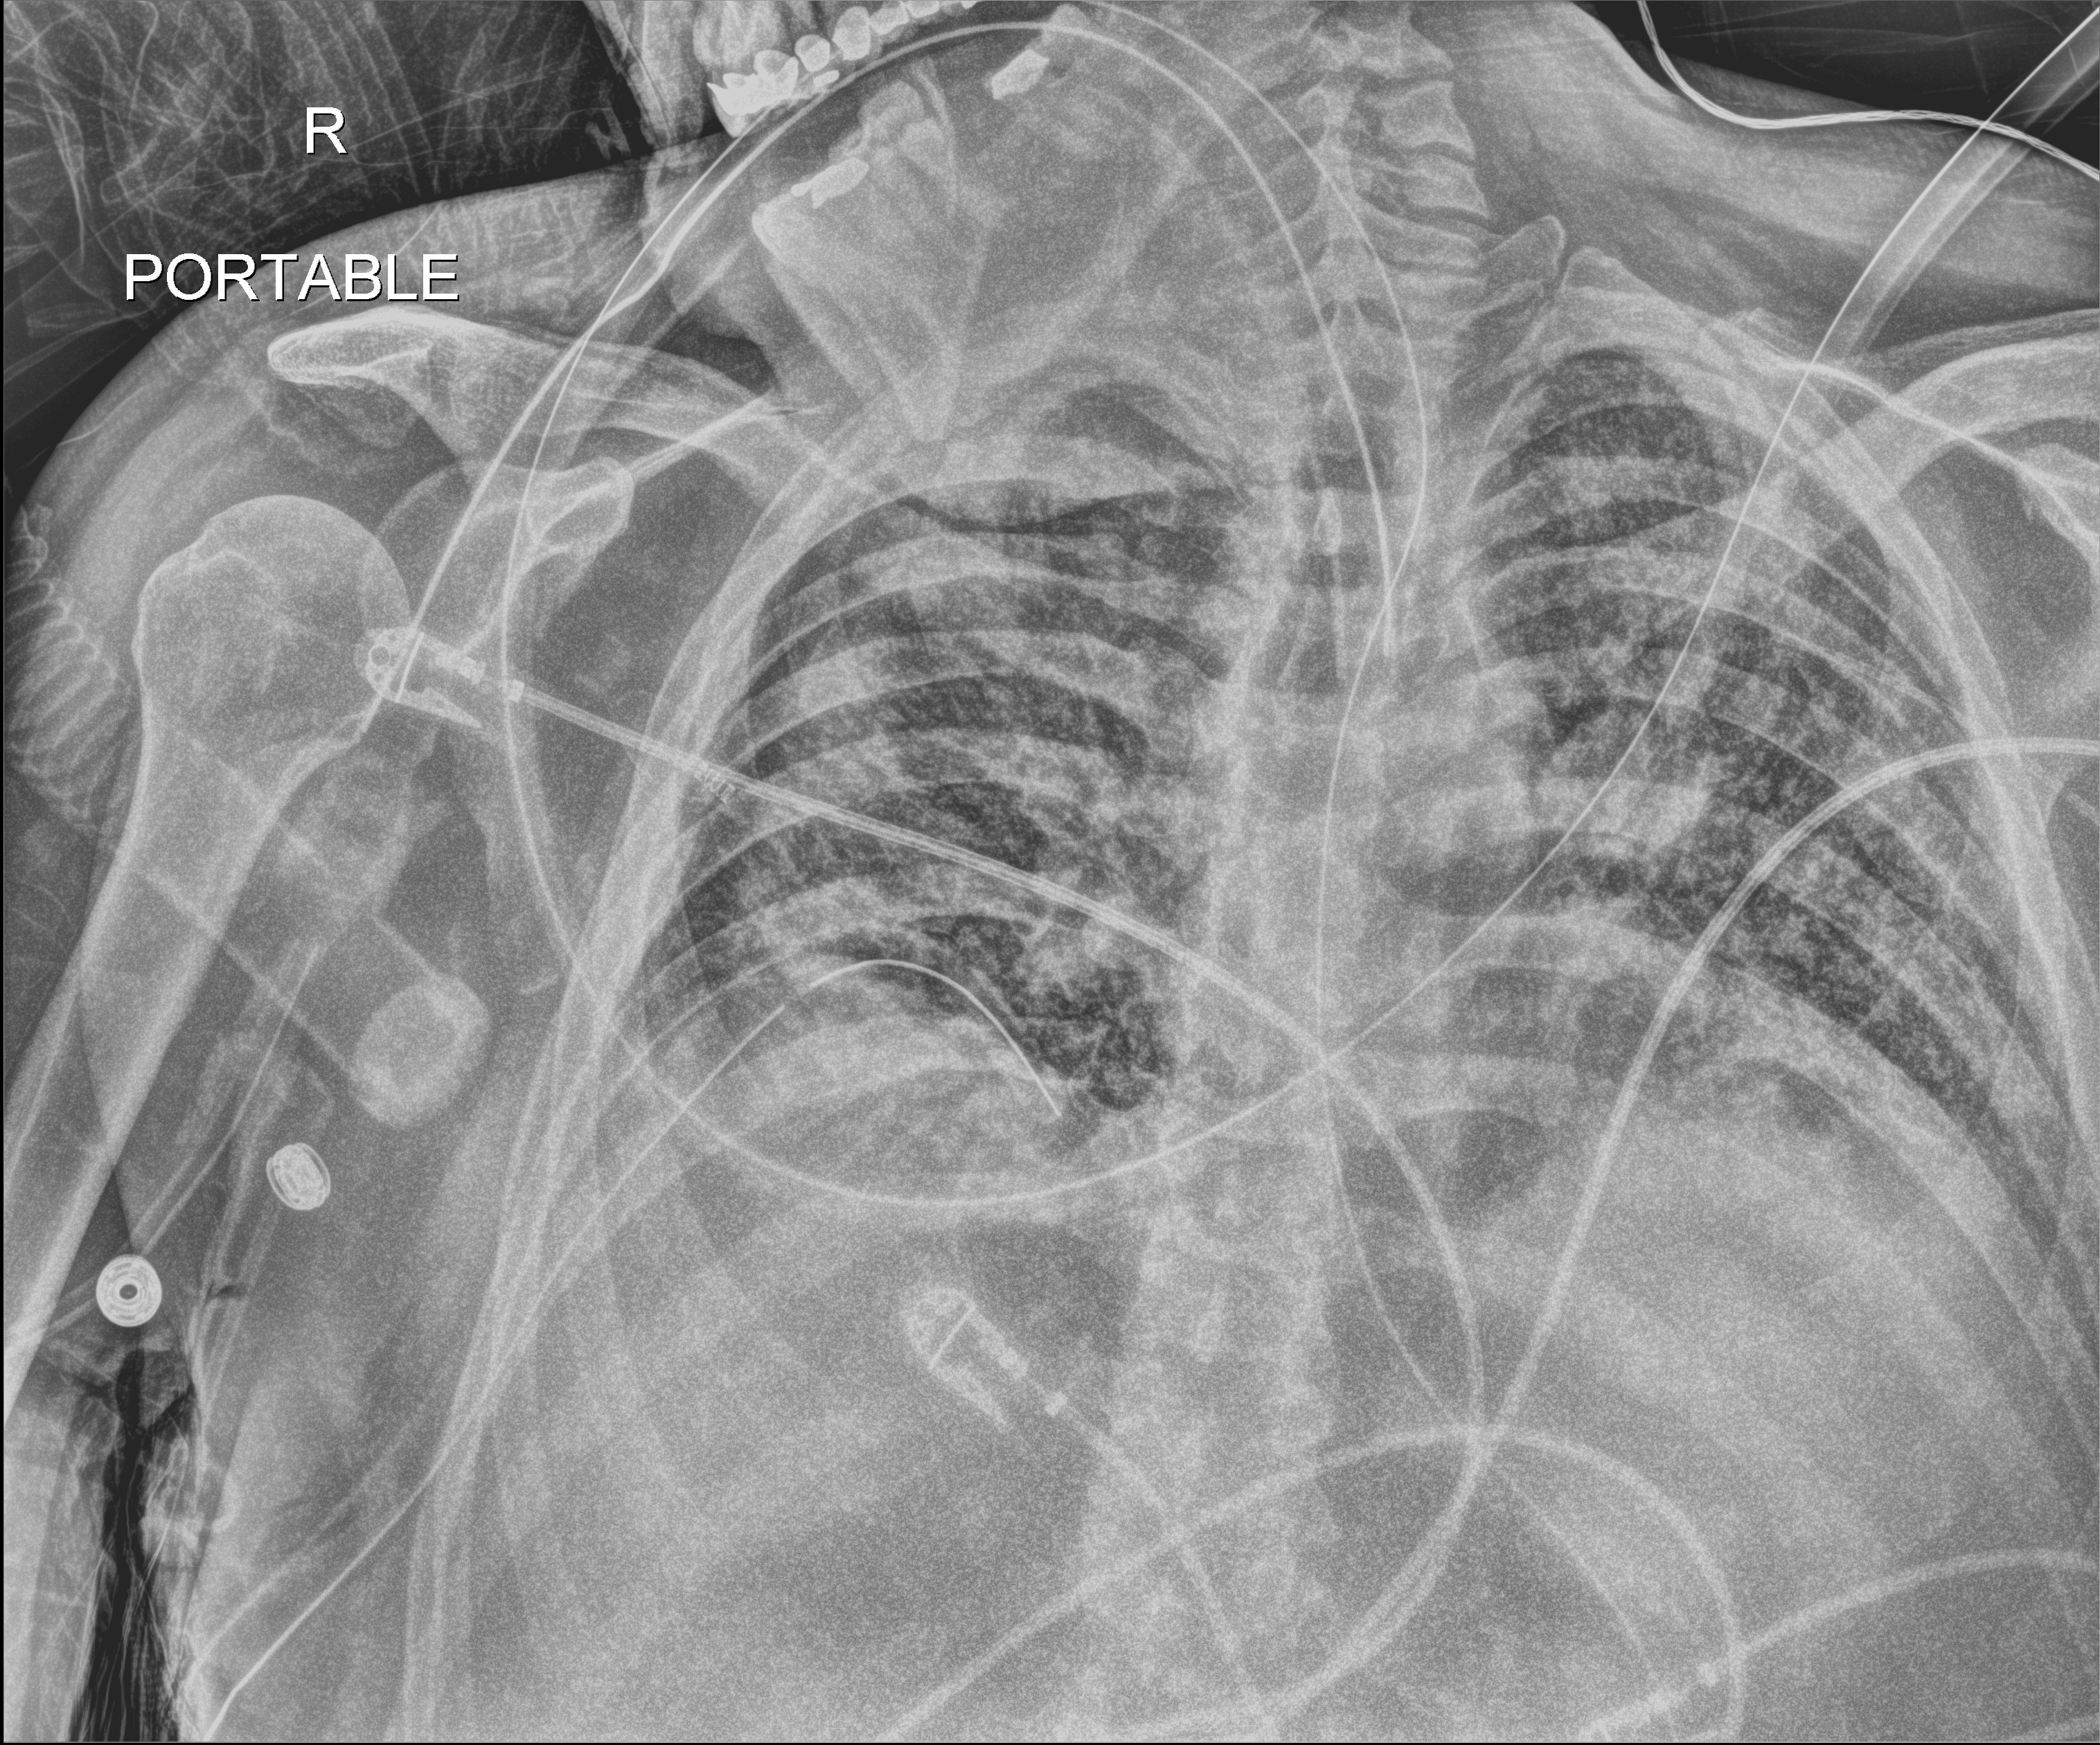
Chest radiograph (digital radiography). Patient hospitalised with COVID-19; male, aged 18–59 years.
From the hospital-stay record, not from the radiograph (when in the stay this image was taken is not recorded):
- length of hospital stay: 80 days
- diabetes (admission record): no
- admitted to intensive care during this hospital stay: yes